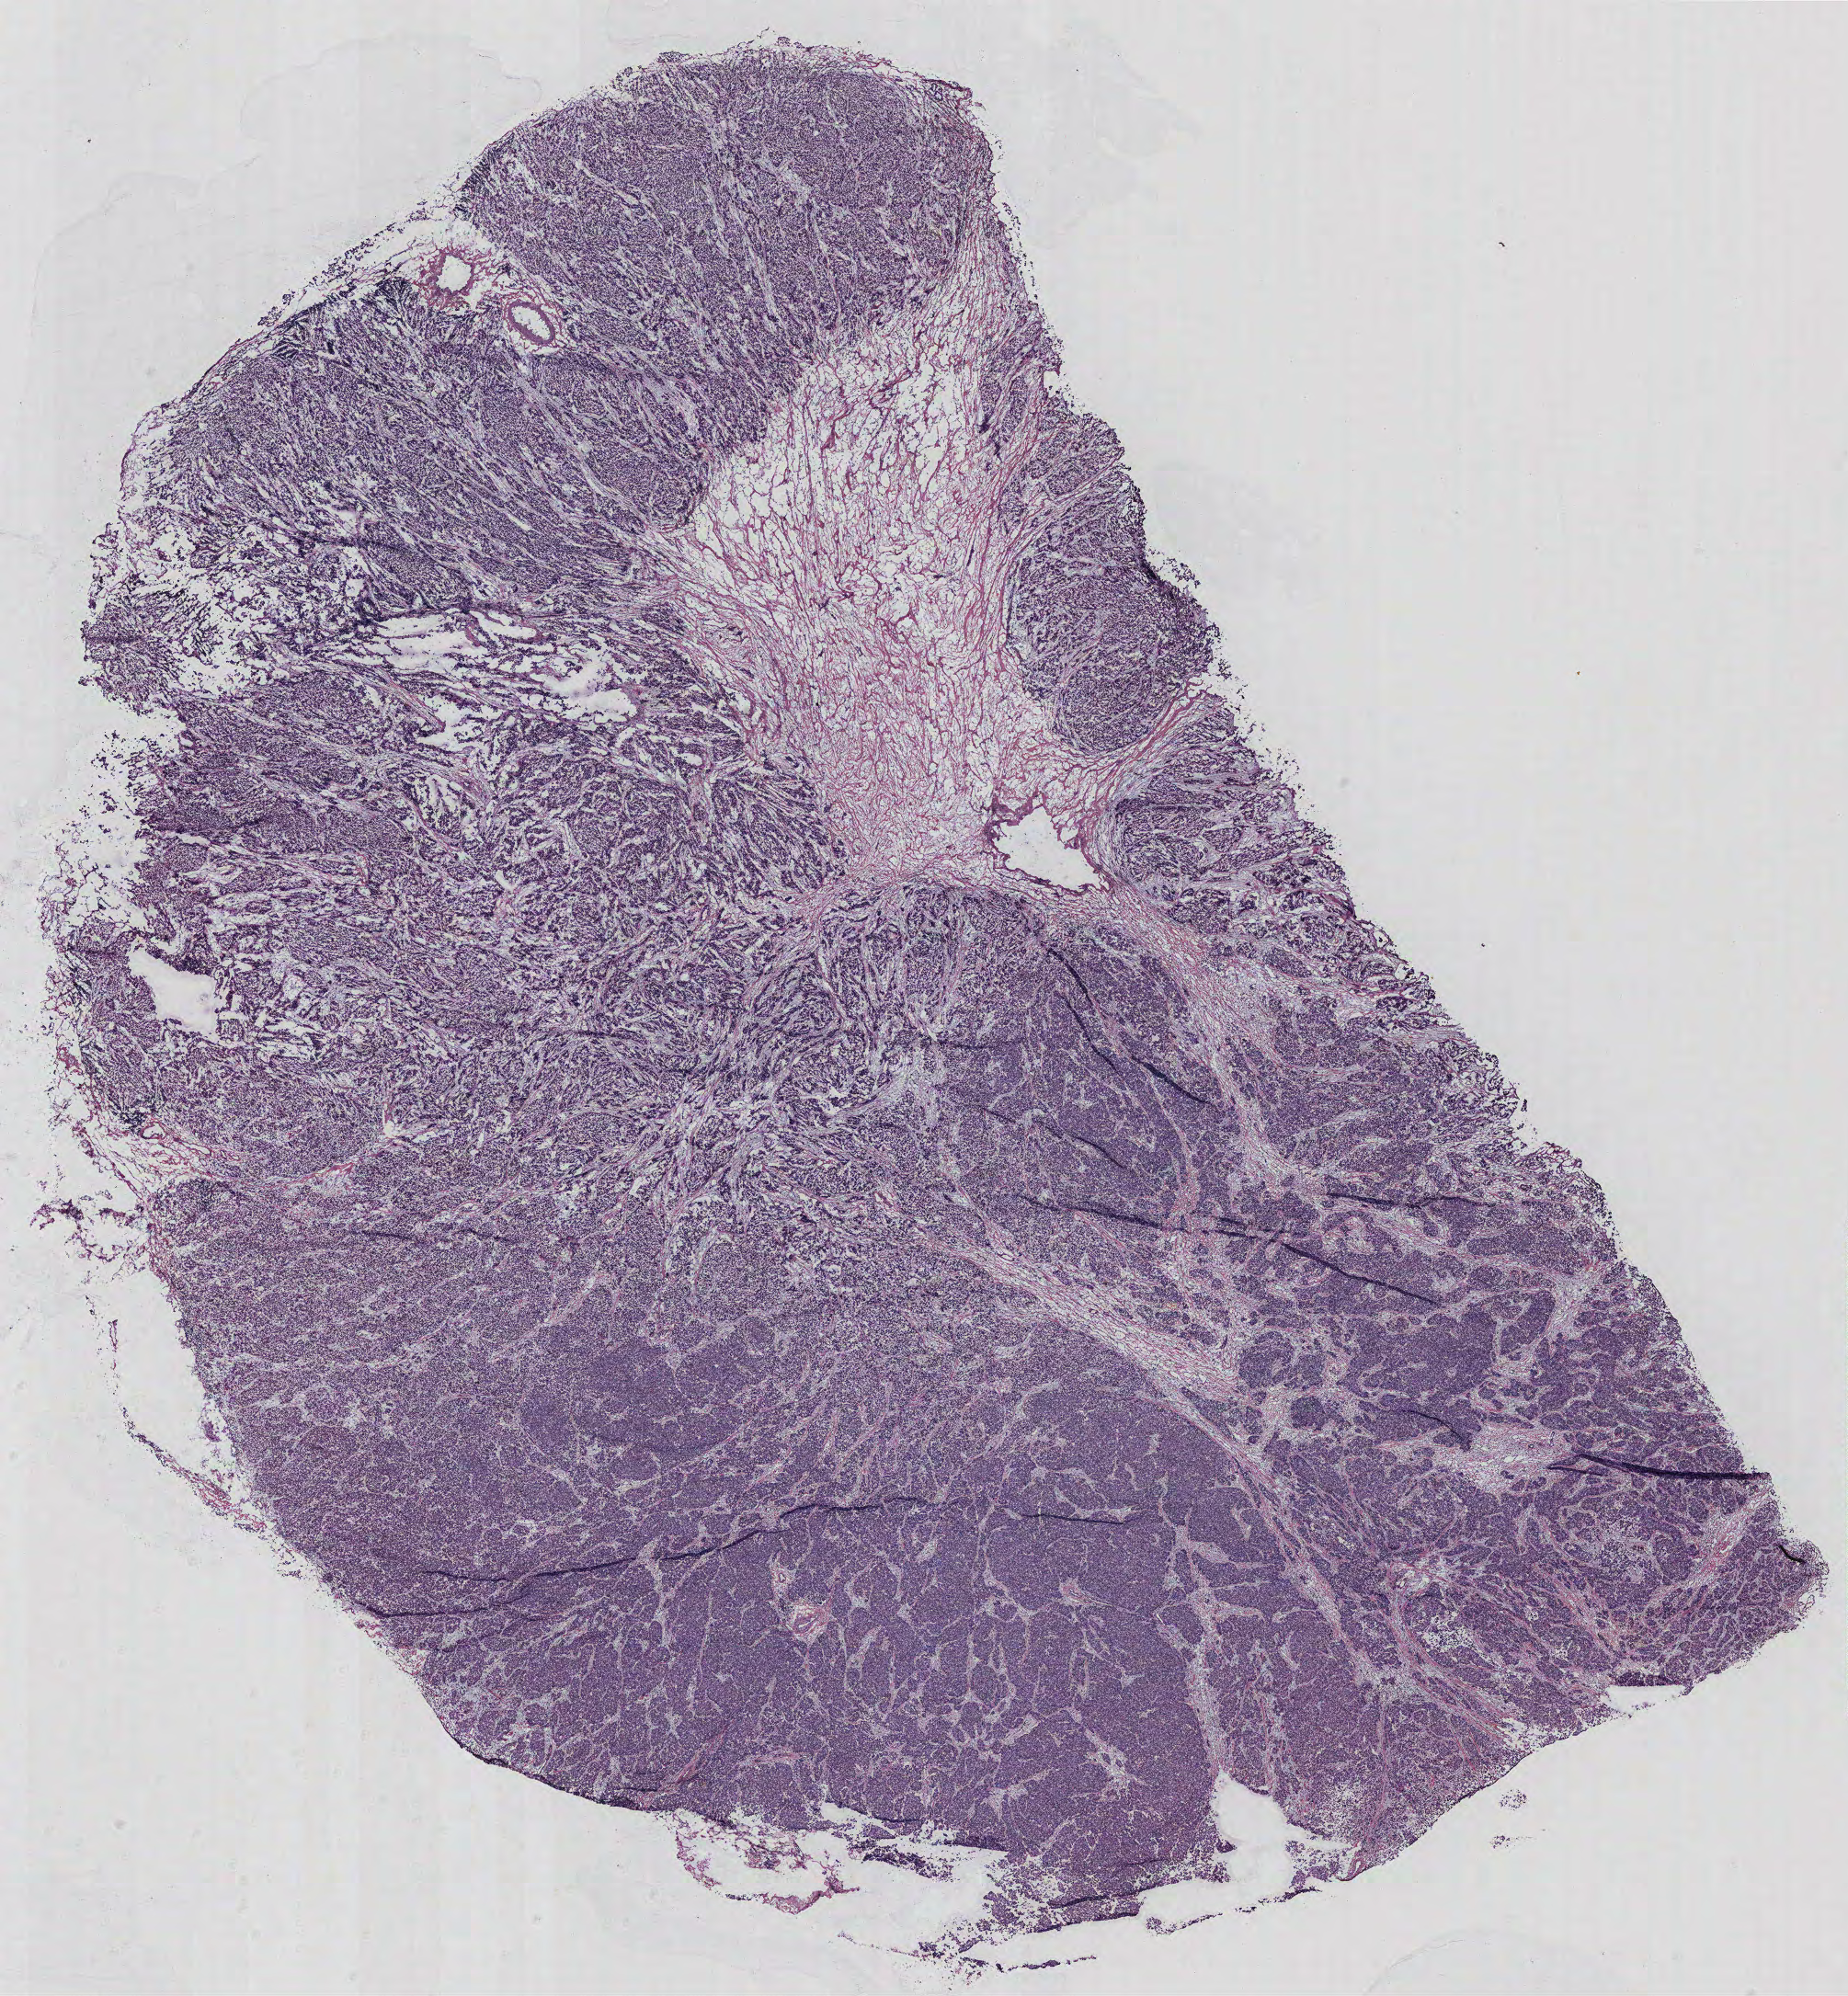
H&E-stained whole-slide image — whole scanned area (about 16.1 x 17.4 mm) shown as a low-resolution overview. Breast, tissue type not recorded.
• patient diagnosis (cohort enrolment): breast cancer (breast)